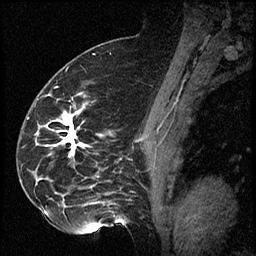
Breast MRI (dynamic contrast-enhanced), one sagittal slice; position 42 of 60 along the scan axis; dynamic contrast-enhanced series, image 2 of 2 at this slice position (ordered by acquisition); 1.5 T; TE 4.2 ms, TR 17.3 ms; 2 mm slice thickness; 256 × 256 image matrix. Female patient. Case-level facts recorded for this patient, not image findings: setting: breast cancer imaged before/during neoadjuvant chemotherapy; receptor status: HR-positive, HER2-negative.
Outlined on this slice (semi-automatically segmented with operator editing):
- analysis volume of interest (the breast-tissue region the enhancement analysis was run in; not a lesion): bounding box <41,98,115,223> (left, top, right, bottom; pixels)
- tumour enhancement mask (voxels above the 100 % enhancement threshold inside the analysis volume of interest): <63,110,81,153>